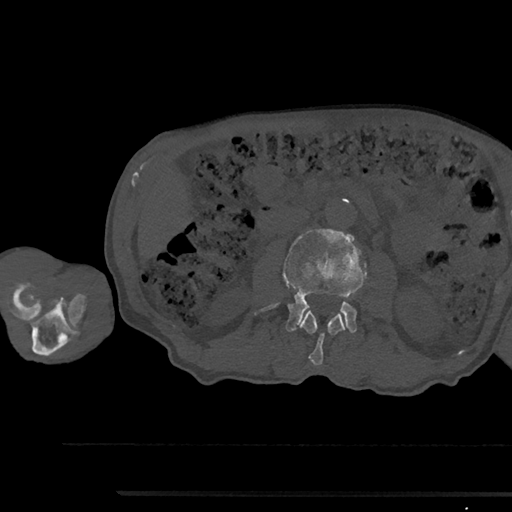
CT including the spine, one axial slice. Position 522 of 797 along the scan axis. Reconstruction kernel Br40s/3. 120 kVp. Bone window (W 1800 / L 400 HU). 512 × 512 image matrix. Male patient, age 79 years. From the clinical record (not read from this slice): primary cancer: prostate.
Outlined on this slice (semi-automatically segmented with operator editing):
- L2 vertebra: bounding box [x1, y1, x2, y2] px = [299, 310, 345, 365]
- L3 vertebra: [254, 229, 367, 333]